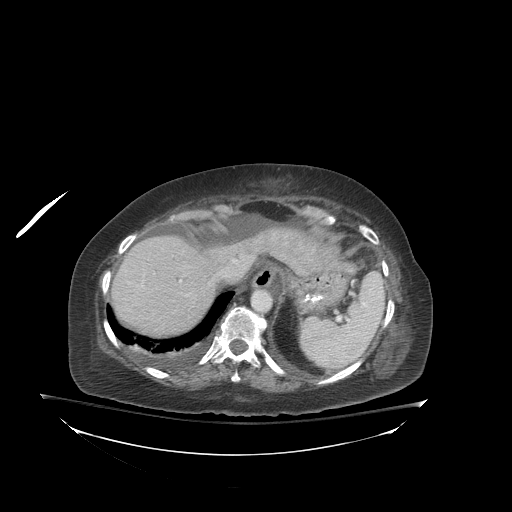
Contrast-enhanced abdominal CT (liver protocol), one axial slice. Position 67 of 81 along the scan axis. 140 kVp. Soft-tissue window (W 400 / L 40 HU). 2.5 mm slice thickness. 512 × 512 image matrix, field of view 500 × 500 mm. From the clinical record (not read from this slice): diagnosis: hepatocellular carcinoma (patient treated with transarterial chemoembolisation; whether this scan precedes or follows treatment is not stated here); TNM stage (as recorded): Stage-I; Child-Pugh class: B.
Annotated regions visible in this slice (semi-automatically segmented with operator editing):
- liver parenchyma outside the tumour (the mass and vessels are separate outlines, so this box may not span the whole liver): box from (x=112, y=230) to (x=281, y=336) px
- liver vessels: (x=180, y=261)–(x=236, y=282)